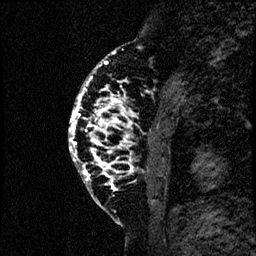
Breast MRI (dynamic contrast-enhanced), one sagittal slice; position 22 of 60 along the scan axis; dynamic contrast-enhanced study with each time point stored as its own series, time point 2 of 4 at this slice position (early post-contrast, ordered by acquisition time); 1.5 T; TE 4.2 ms, TR 17.6 ms; 2 mm slice thickness; 256 × 256 image matrix, field of view 200 × 200 mm. Female patient, age 40 years. From the clinical record (not read from this slice): setting: breast cancer imaged before/during neoadjuvant chemotherapy; receptor status: HER2-positive.
Structures marked on this image (semi-automatic segmentation, software-assisted and operator-edited):
- analysis volume of interest (the breast-tissue region the enhancement analysis was run in; not a lesion): box from (x=66, y=55) to (x=185, y=206) px
- tumour enhancement mask (voxels above the 100 % enhancement threshold inside the analysis volume of interest): (x=68, y=64)–(x=129, y=184)